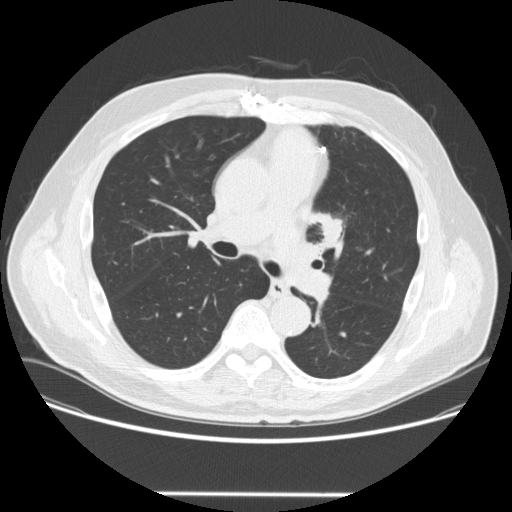
Axial slice from a low-dose chest CT screening exam, third annual screen, lung window (W 1500 / L -600 HU), 2.5 mm slice thickness, standard (soft-tissue) reconstruction kernel (STANDARD), slice 96 of 253 in the series, 512 × 512 image matrix. Male, age 66 years at enrolment.
Lesion marked by an expert reader, bounding box [x1, y1, x2, y2] px = [304, 208, 356, 256]. The screening reader recorded 2 non-calcified nodules or masses ≥4 mm on this exam; which of them this box marks is not recorded. Lung cancer was diagnosed 85 days after this screen: squamous cell carcinoma, NOS, left upper lobe, poorly differentiated (G3), stage IA (AJCC 6th edition), 27 mm at pathology.